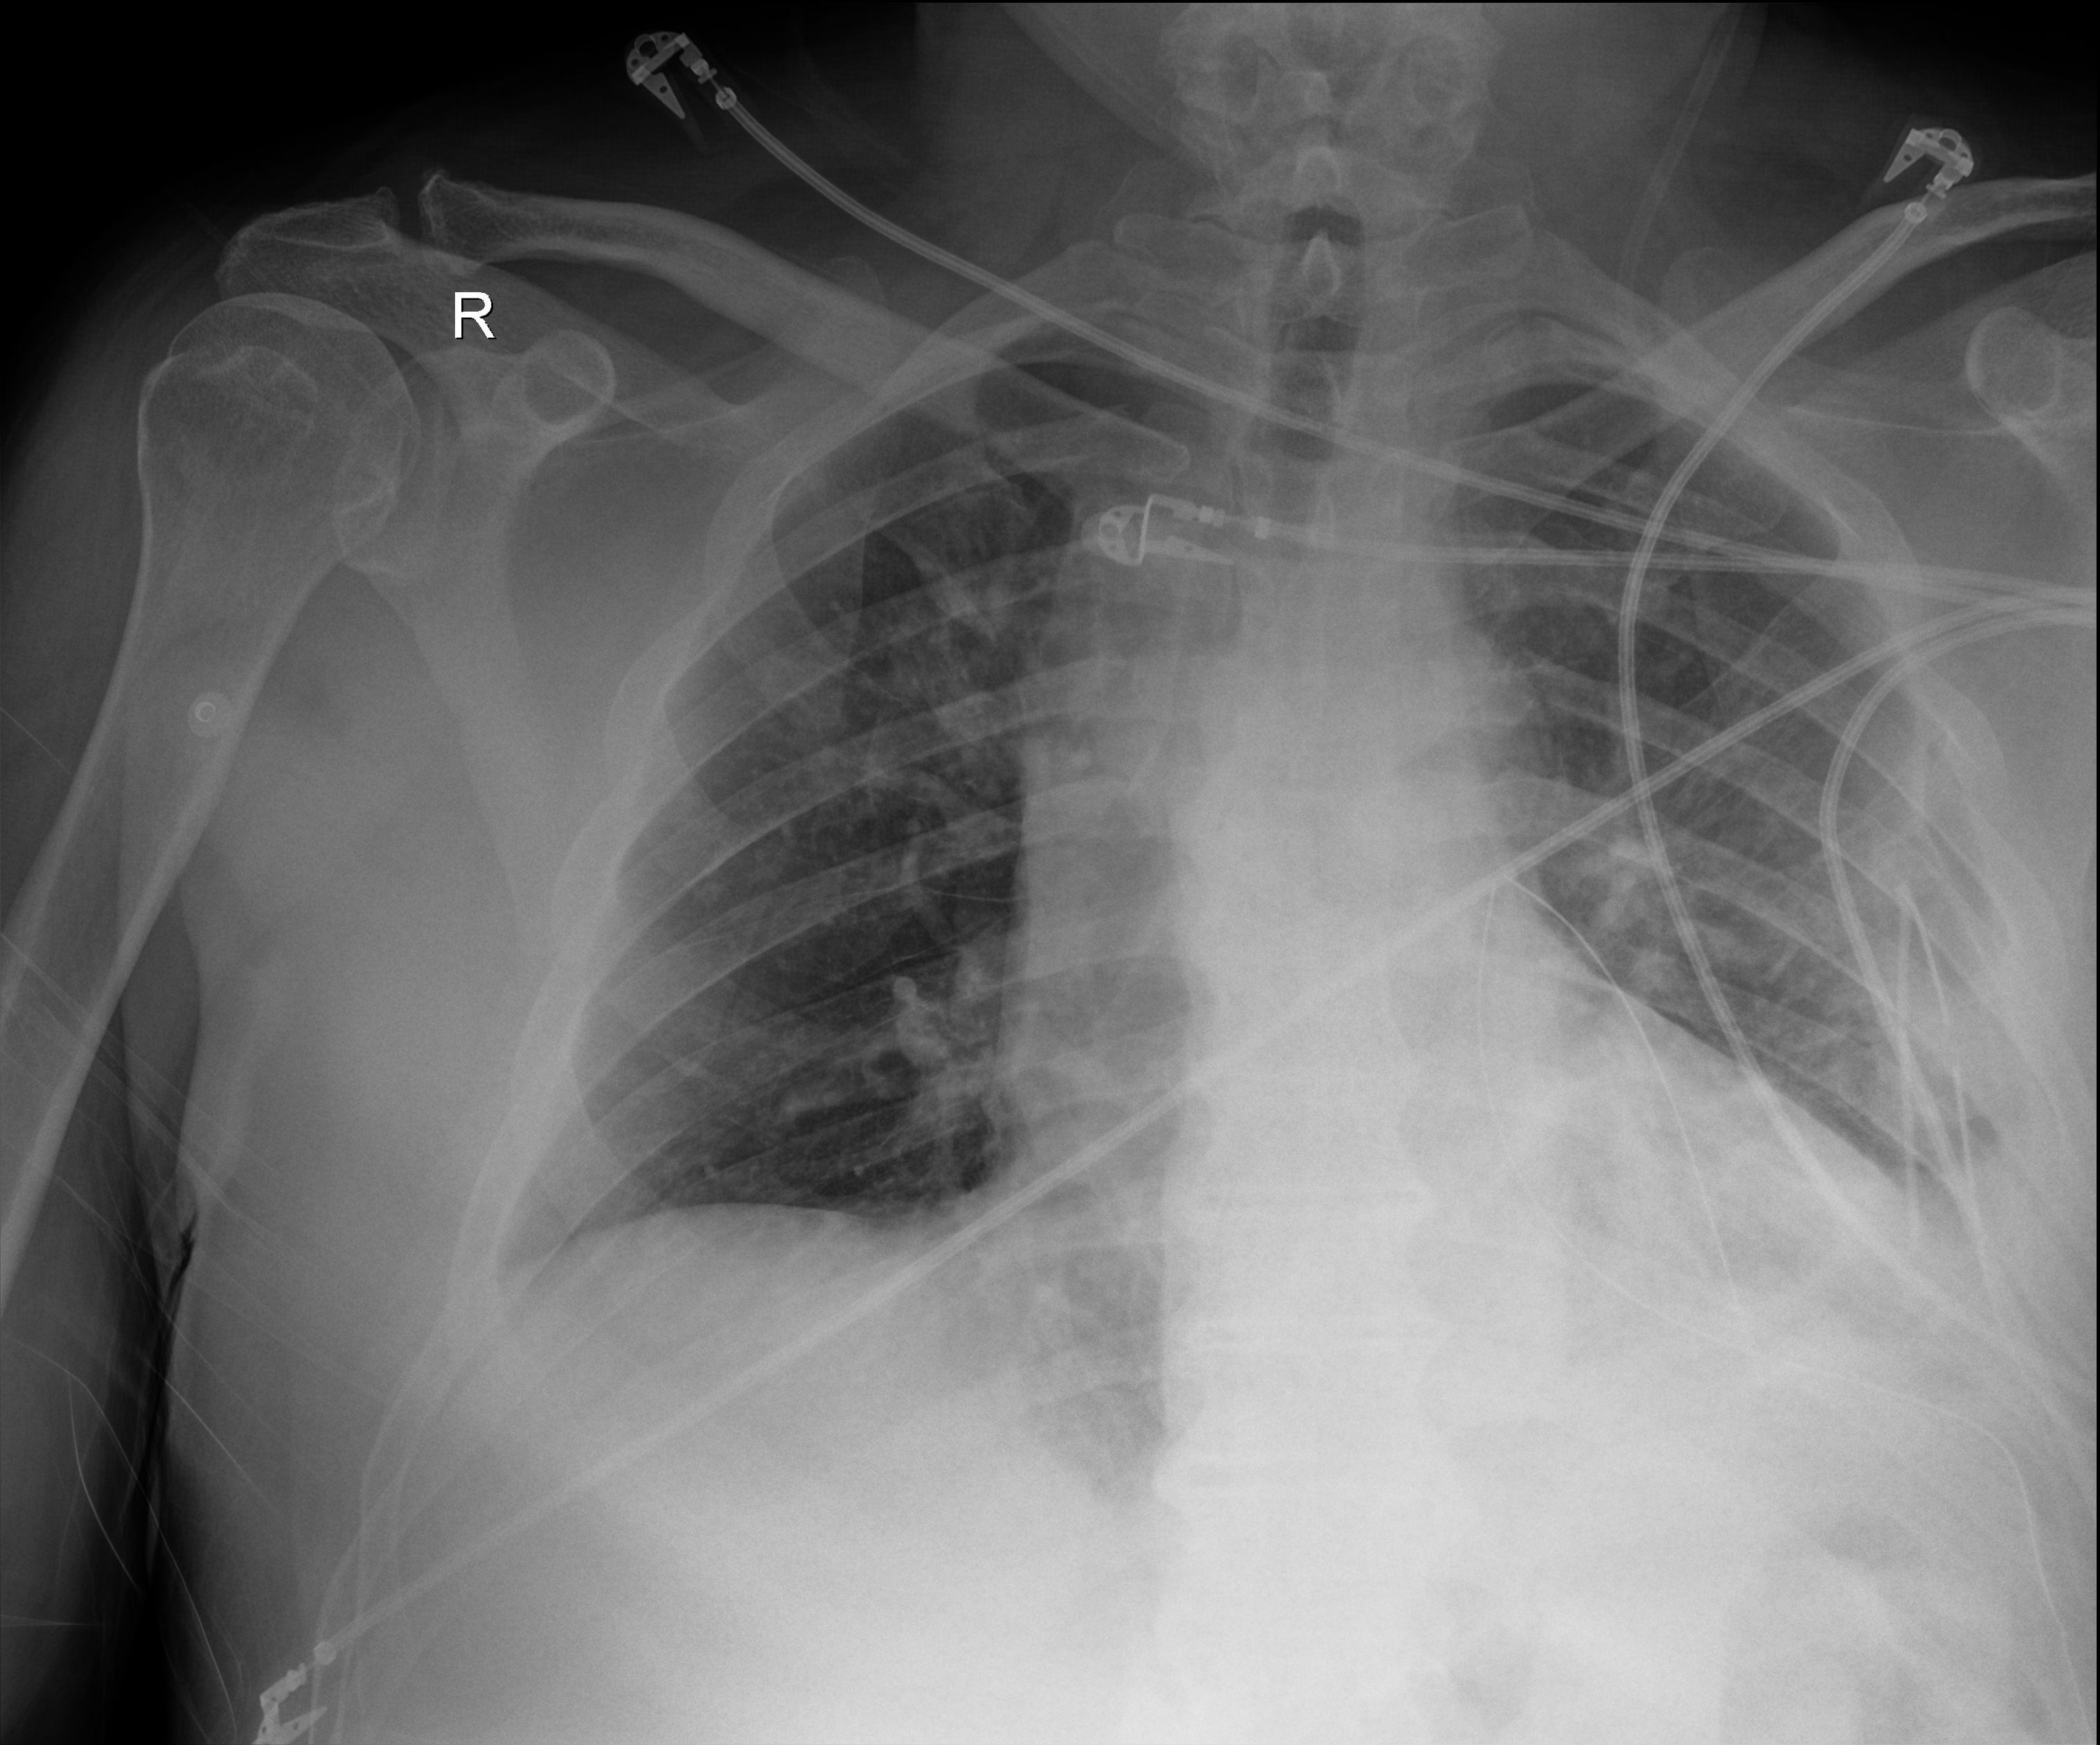
Bedside chest radiograph (digital radiography); anteroposterior (AP) projection. Patient hospitalised with COVID-19; male, aged 18–59 years.
Admission-level facts for this patient (not findings on this image; timing relative to this image not recorded): length of hospital stay: 10 days; mechanically ventilated during this hospital stay: no.